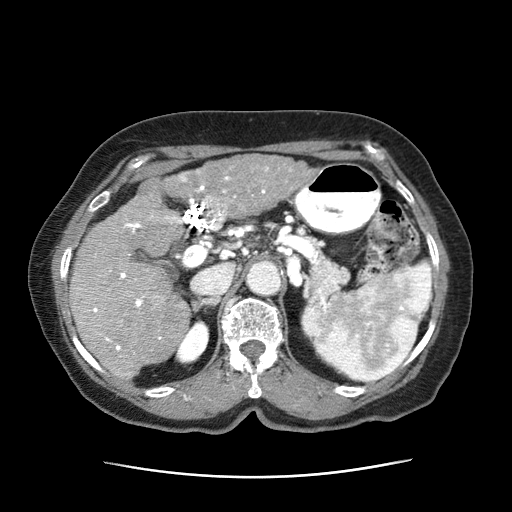
Contrast-enhanced abdominal CT (liver protocol), one axial slice; position 34 of 63 along the scan axis; reconstruction kernel STANDARD; 120 kVp; intravenous contrast given; soft-tissue window (W 400 / L 40 HU); 2.5 mm slice thickness; 512 × 512 image matrix, field of view 360 × 360 mm. Female patient, age 79 years. From the clinical record (not read from this slice): diagnosis: hepatocellular carcinoma (patient treated with transarterial chemoembolisation; whether this scan precedes or follows treatment is not stated here); TNM stage (as recorded): Stage-II; Child-Pugh class: B; tumour differentiation: well differentiated; tumour nodularity: multinodular.
Outlined on this slice (semi-automatically segmented with operator editing):
- abdominal aorta: bounding box <247,260,282,296> (left, top, right, bottom; pixels)
- liver parenchyma outside the tumour (the mass and vessels are separate outlines, so this box may not span the whole liver): <68,175,191,381>
- mass: <161,155,319,218>
- liver vessels: <87,176,266,355>